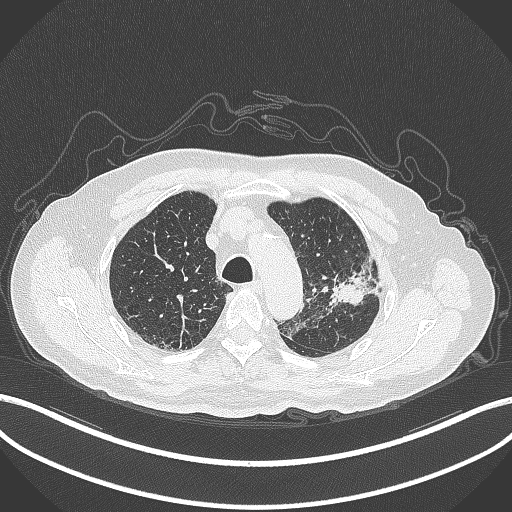
Chest CT, one axial slice. Position 229 of 331 along the scan axis. Reconstruction kernel B70f. 120 kVp. Lung window (W 1500 / L -600 HU). 1 mm slice thickness. 512 × 512 image matrix. Patient: male, 79 years. From the clinical record (not read from this slice): clinical TNM (as recorded): T2a N1 M1; histopathological grade: G3.
Structures marked on this image (rectangle marked by the reading radiologist):
- lung tumour (recorded histology: adenocarcinoma): bounding box (x1, y1, x2, y2) in pixels: (324, 251, 380, 311)